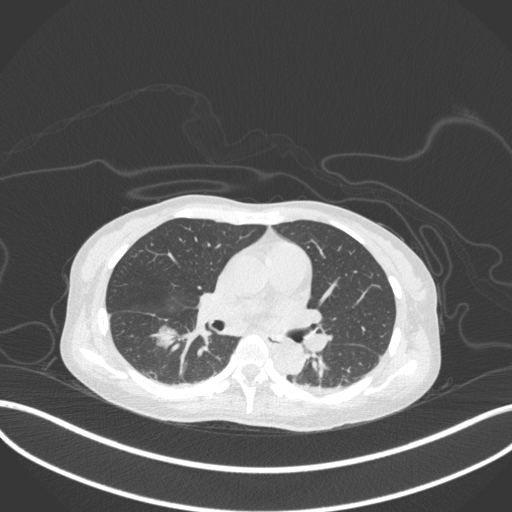
Chest CT, one axial slice; position 167 of 260 along the scan axis; 120 kVp; lung window (W 1500 / L -600 HU); 1 mm slice thickness; 512 × 512 image matrix, field of view 400 × 400 mm. Female patient, age 44 years. Case-level facts recorded for this patient, not image findings: clinical TNM (as recorded): T1c N0 M0.
Outlined on this slice (rectangle marked by the reading radiologist):
- lung tumour (recorded histology: adenocarcinoma): box from (x=148, y=320) to (x=179, y=357) px